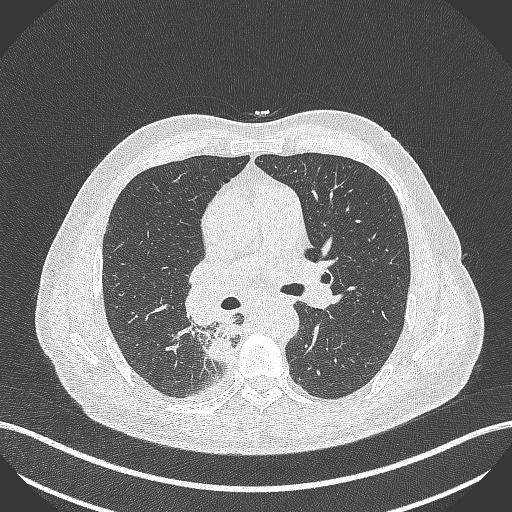
Chest CT, one axial slice. Position 271 of 451 along the scan axis. Reconstruction kernel B70f. Lung window (W 1500 / L -600 HU). 1 mm slice thickness. 512 × 512 image matrix, field of view 400 × 400 mm. Patient: male, 61 years. Case-level facts recorded for this patient, not image findings: clinical TNM (as recorded): T1 N0 M0.
Outlined on this slice (rectangle marked by the reading radiologist):
- lung tumour (recorded histology: small cell carcinoma): bounding box (x1, y1, x2, y2) in pixels: (205, 318, 244, 371)